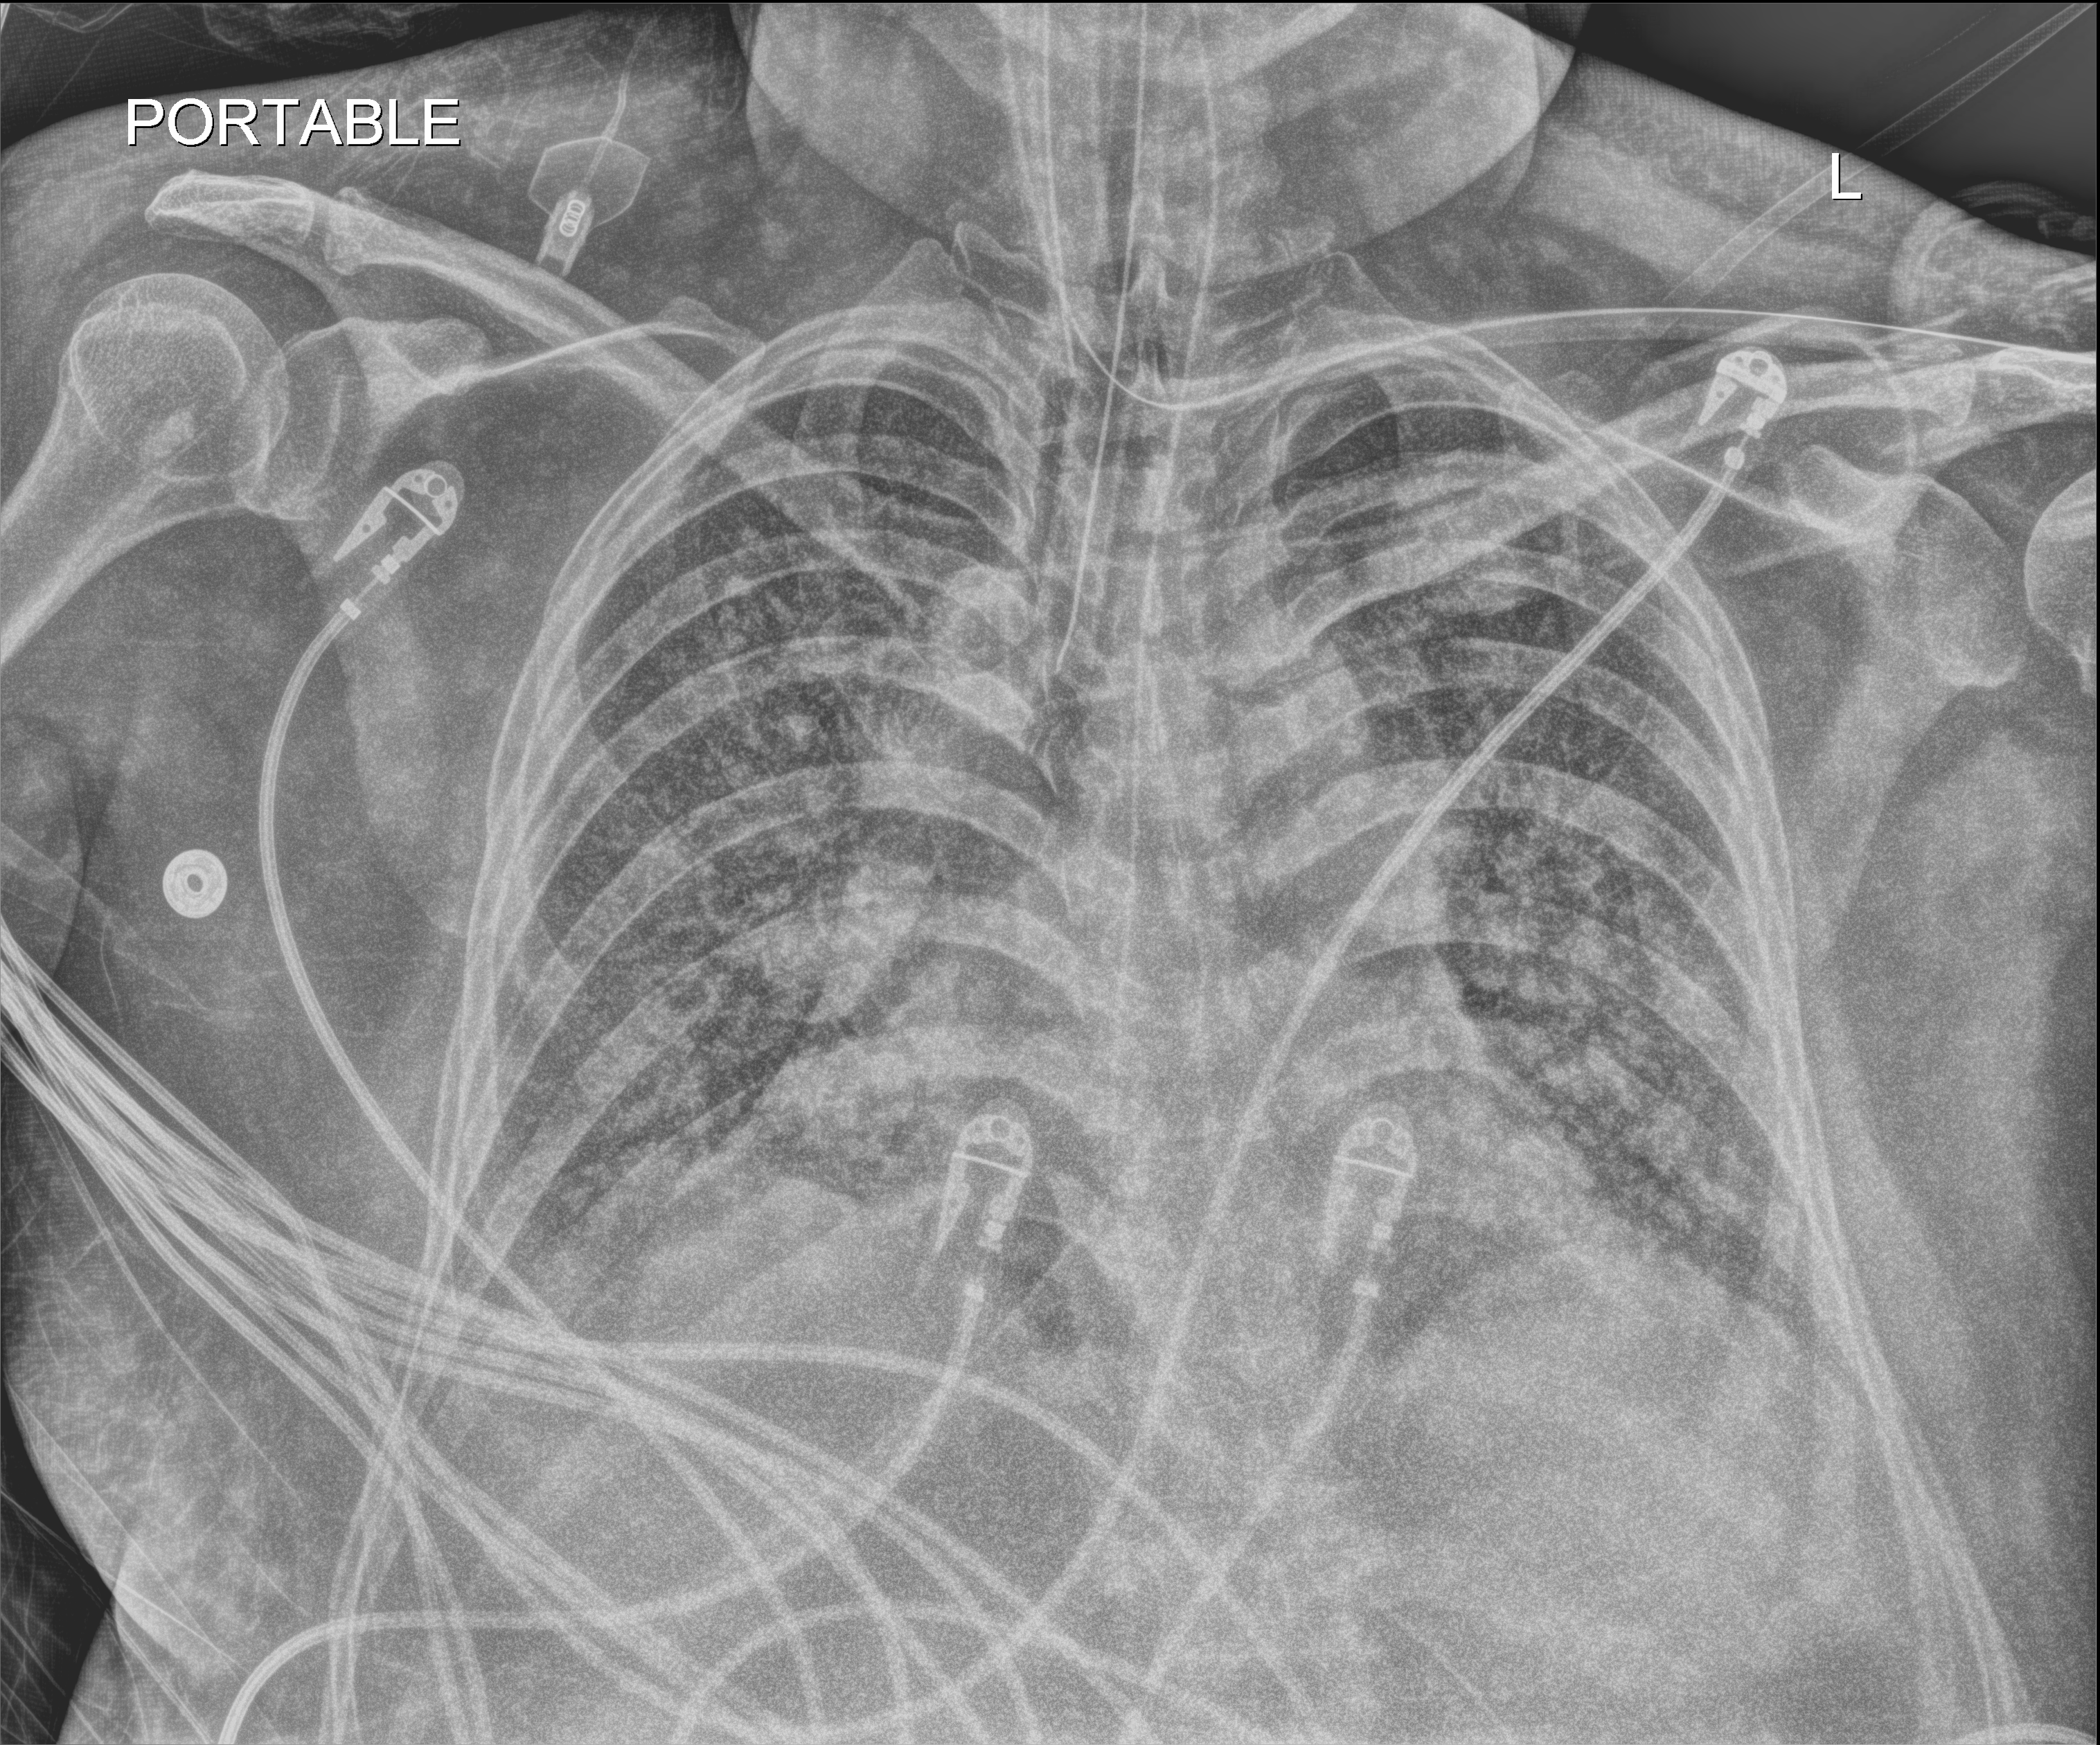
Bedside chest radiograph (digital radiography), anteroposterior (AP) projection. Patient hospitalised with COVID-19, aged 18–59 years.
Admission-level facts for this patient (not findings on this image; timing relative to this image not recorded): smoking status (admission record): never.